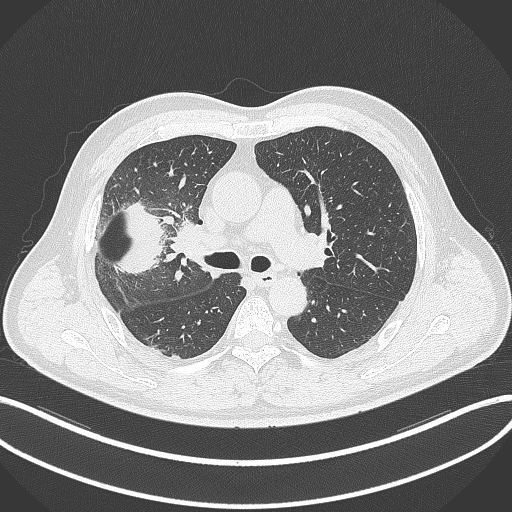
Chest CT, one axial slice. Position 206 of 348 along the scan axis. Reconstruction kernel B70f. Lung window (W 1500 / L -600 HU). 1 mm slice thickness. 512 × 512 image matrix, field of view 400 × 400 mm. Male patient, age 55 years. From the clinical record (not read from this slice): clinical TNM (as recorded): T3 N2 M1.
Annotated regions visible in this slice (rectangle marked by the reading radiologist):
- lung tumour (recorded histology: adenocarcinoma): bounding box <103,195,166,274> (left, top, right, bottom; pixels)